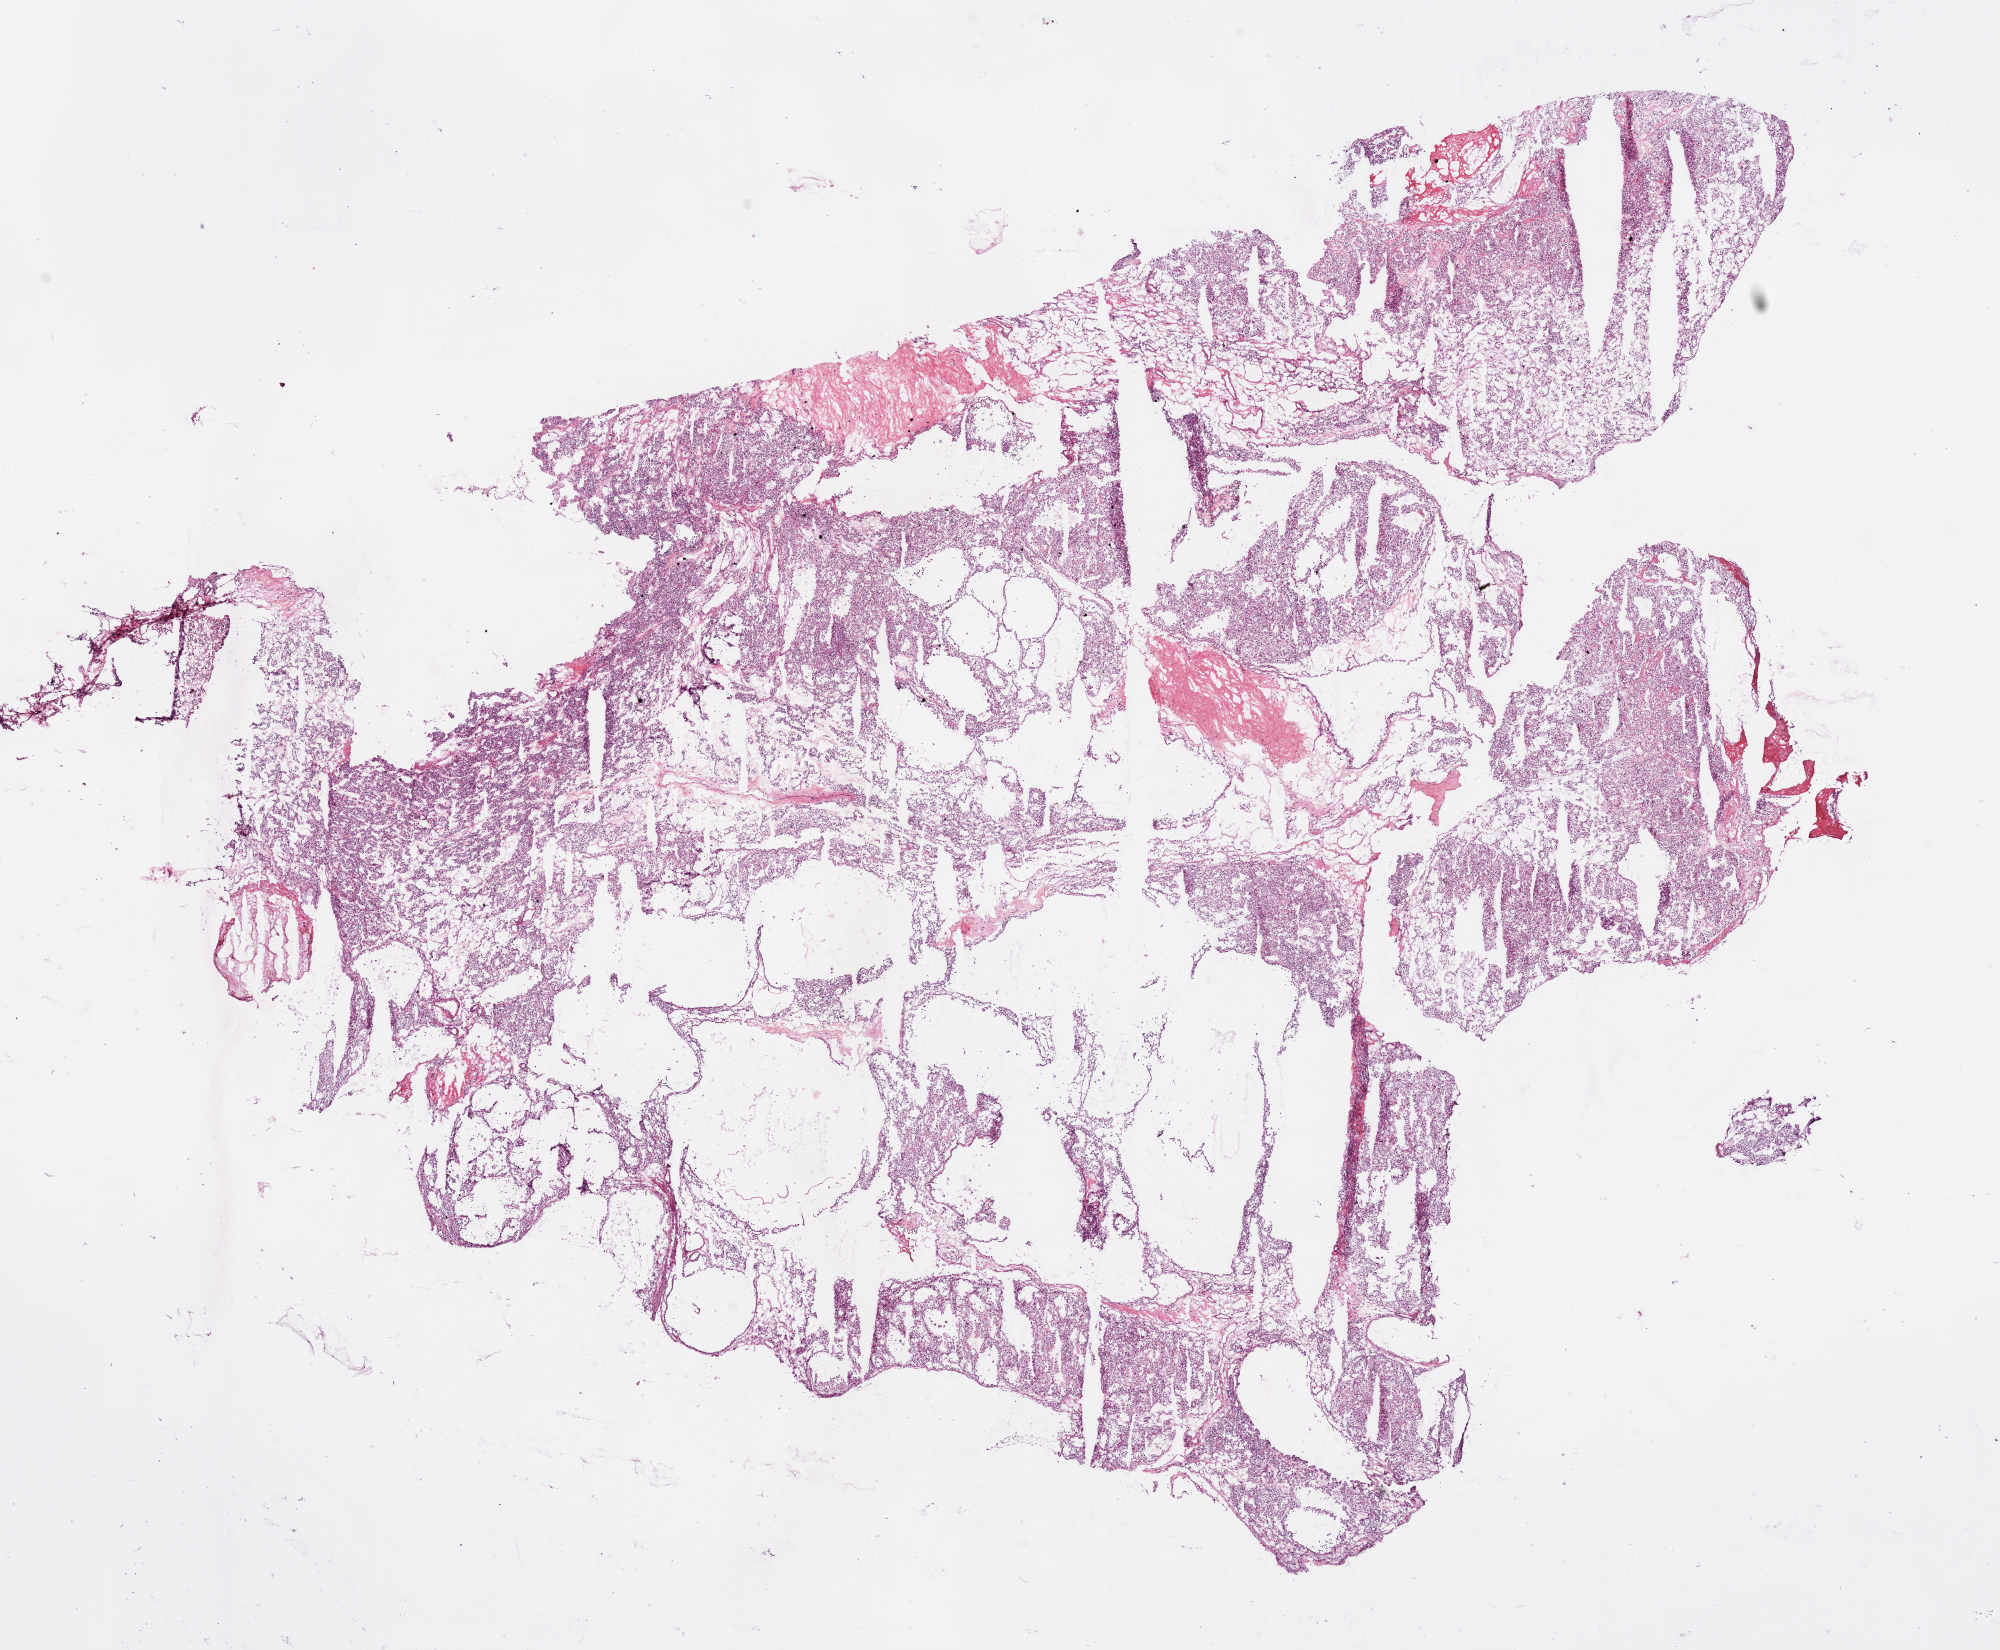
Hematoxylin and eosin (H&E) stained whole-slide image — shown as a low-resolution overview of the whole scanned area (about 16.0 x 13.2 mm, slide scanned at 20x); frozen section; primary tumour sample from the kidney. Patient: male, age at initial diagnosis 58 years. Slide review estimates, as recorded: tumour cells 85%, tumour nuclei 80%.
Histologic diagnosis: Clear cell adenocarcinoma, NOS.